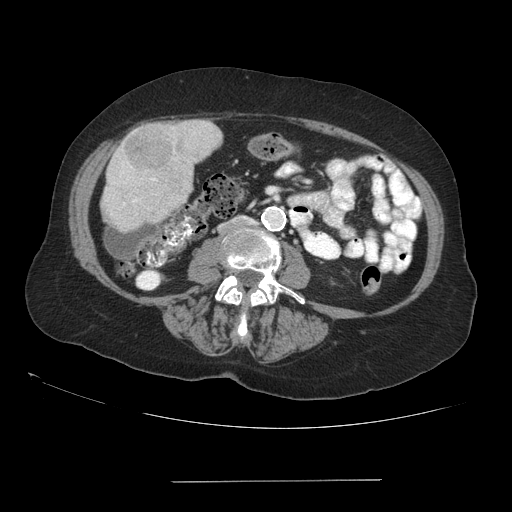
Contrast-enhanced abdominal CT (liver protocol), one axial slice. Reconstruction kernel STANDARD. Soft-tissue window (W 400 / L 40 HU). 2.5 mm slice thickness. 512 × 512 image matrix, field of view 400 × 400 mm. From the clinical record (not read from this slice): diagnosis: hepatocellular carcinoma (patient treated with transarterial chemoembolisation; whether this scan precedes or follows treatment is not stated here); TNM stage (as recorded): Stage-IVA; Child-Pugh class: A; tumour differentiation: poorly differentiated; tumour nodularity: uninodular.
Structures marked on this image (semi-automatic segmentation, software-assisted and operator-edited):
- liver parenchyma outside the tumour (the mass and vessels are separate outlines, so this box may not span the whole liver): bounding box (x1, y1, x2, y2) in pixels: (102, 120, 222, 232)
- mass: (124, 125, 170, 167)